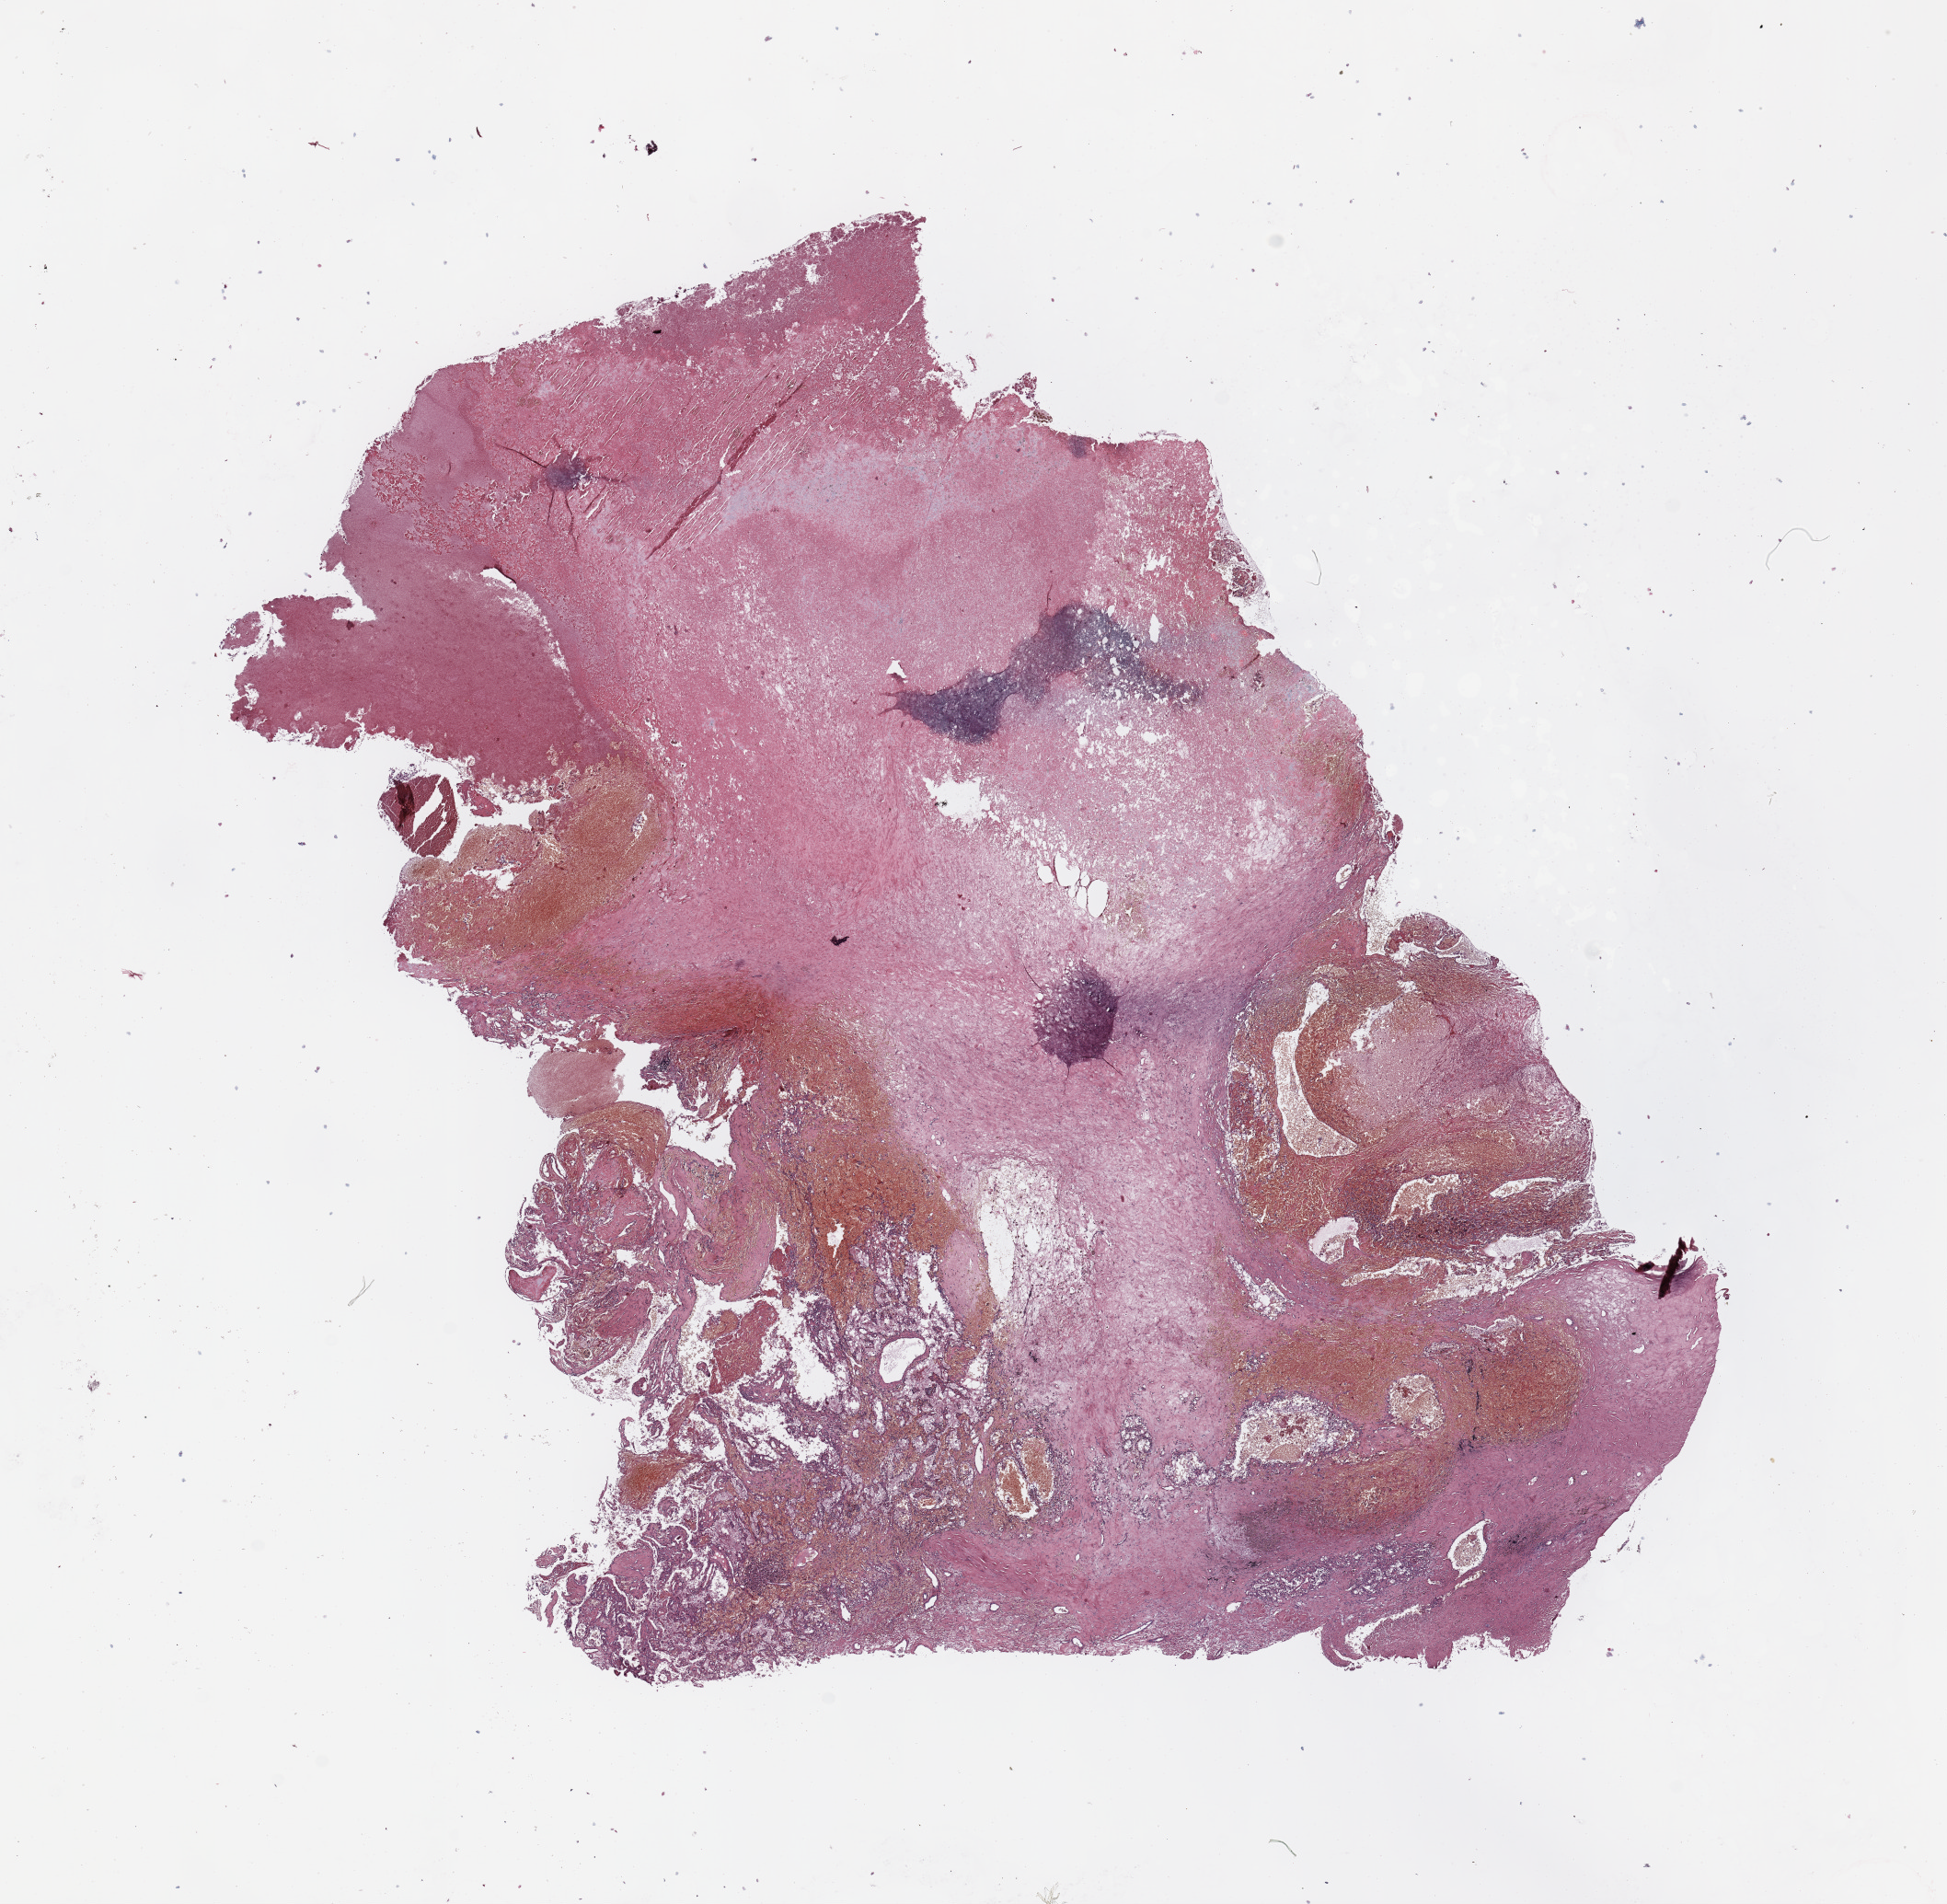
Digitized Hematoxylin and eosin (H&E) stained tissue section (whole slide) — low-resolution overview of the scanned area, about 16.7 x 16.4 mm (from a 20x scan); tumour tissue sample, sampled site: kidney. Patient: male, age 60 years. Histologic grade: G2 (moderately differentiated). Slide review estimates, as recorded: tumour nuclei 50%, necrosis 60%.
* primary tumour site (as recorded): upper pole
* diagnosis: Renal cell carcinoma, NOS
* AJCC pathologic stage: II